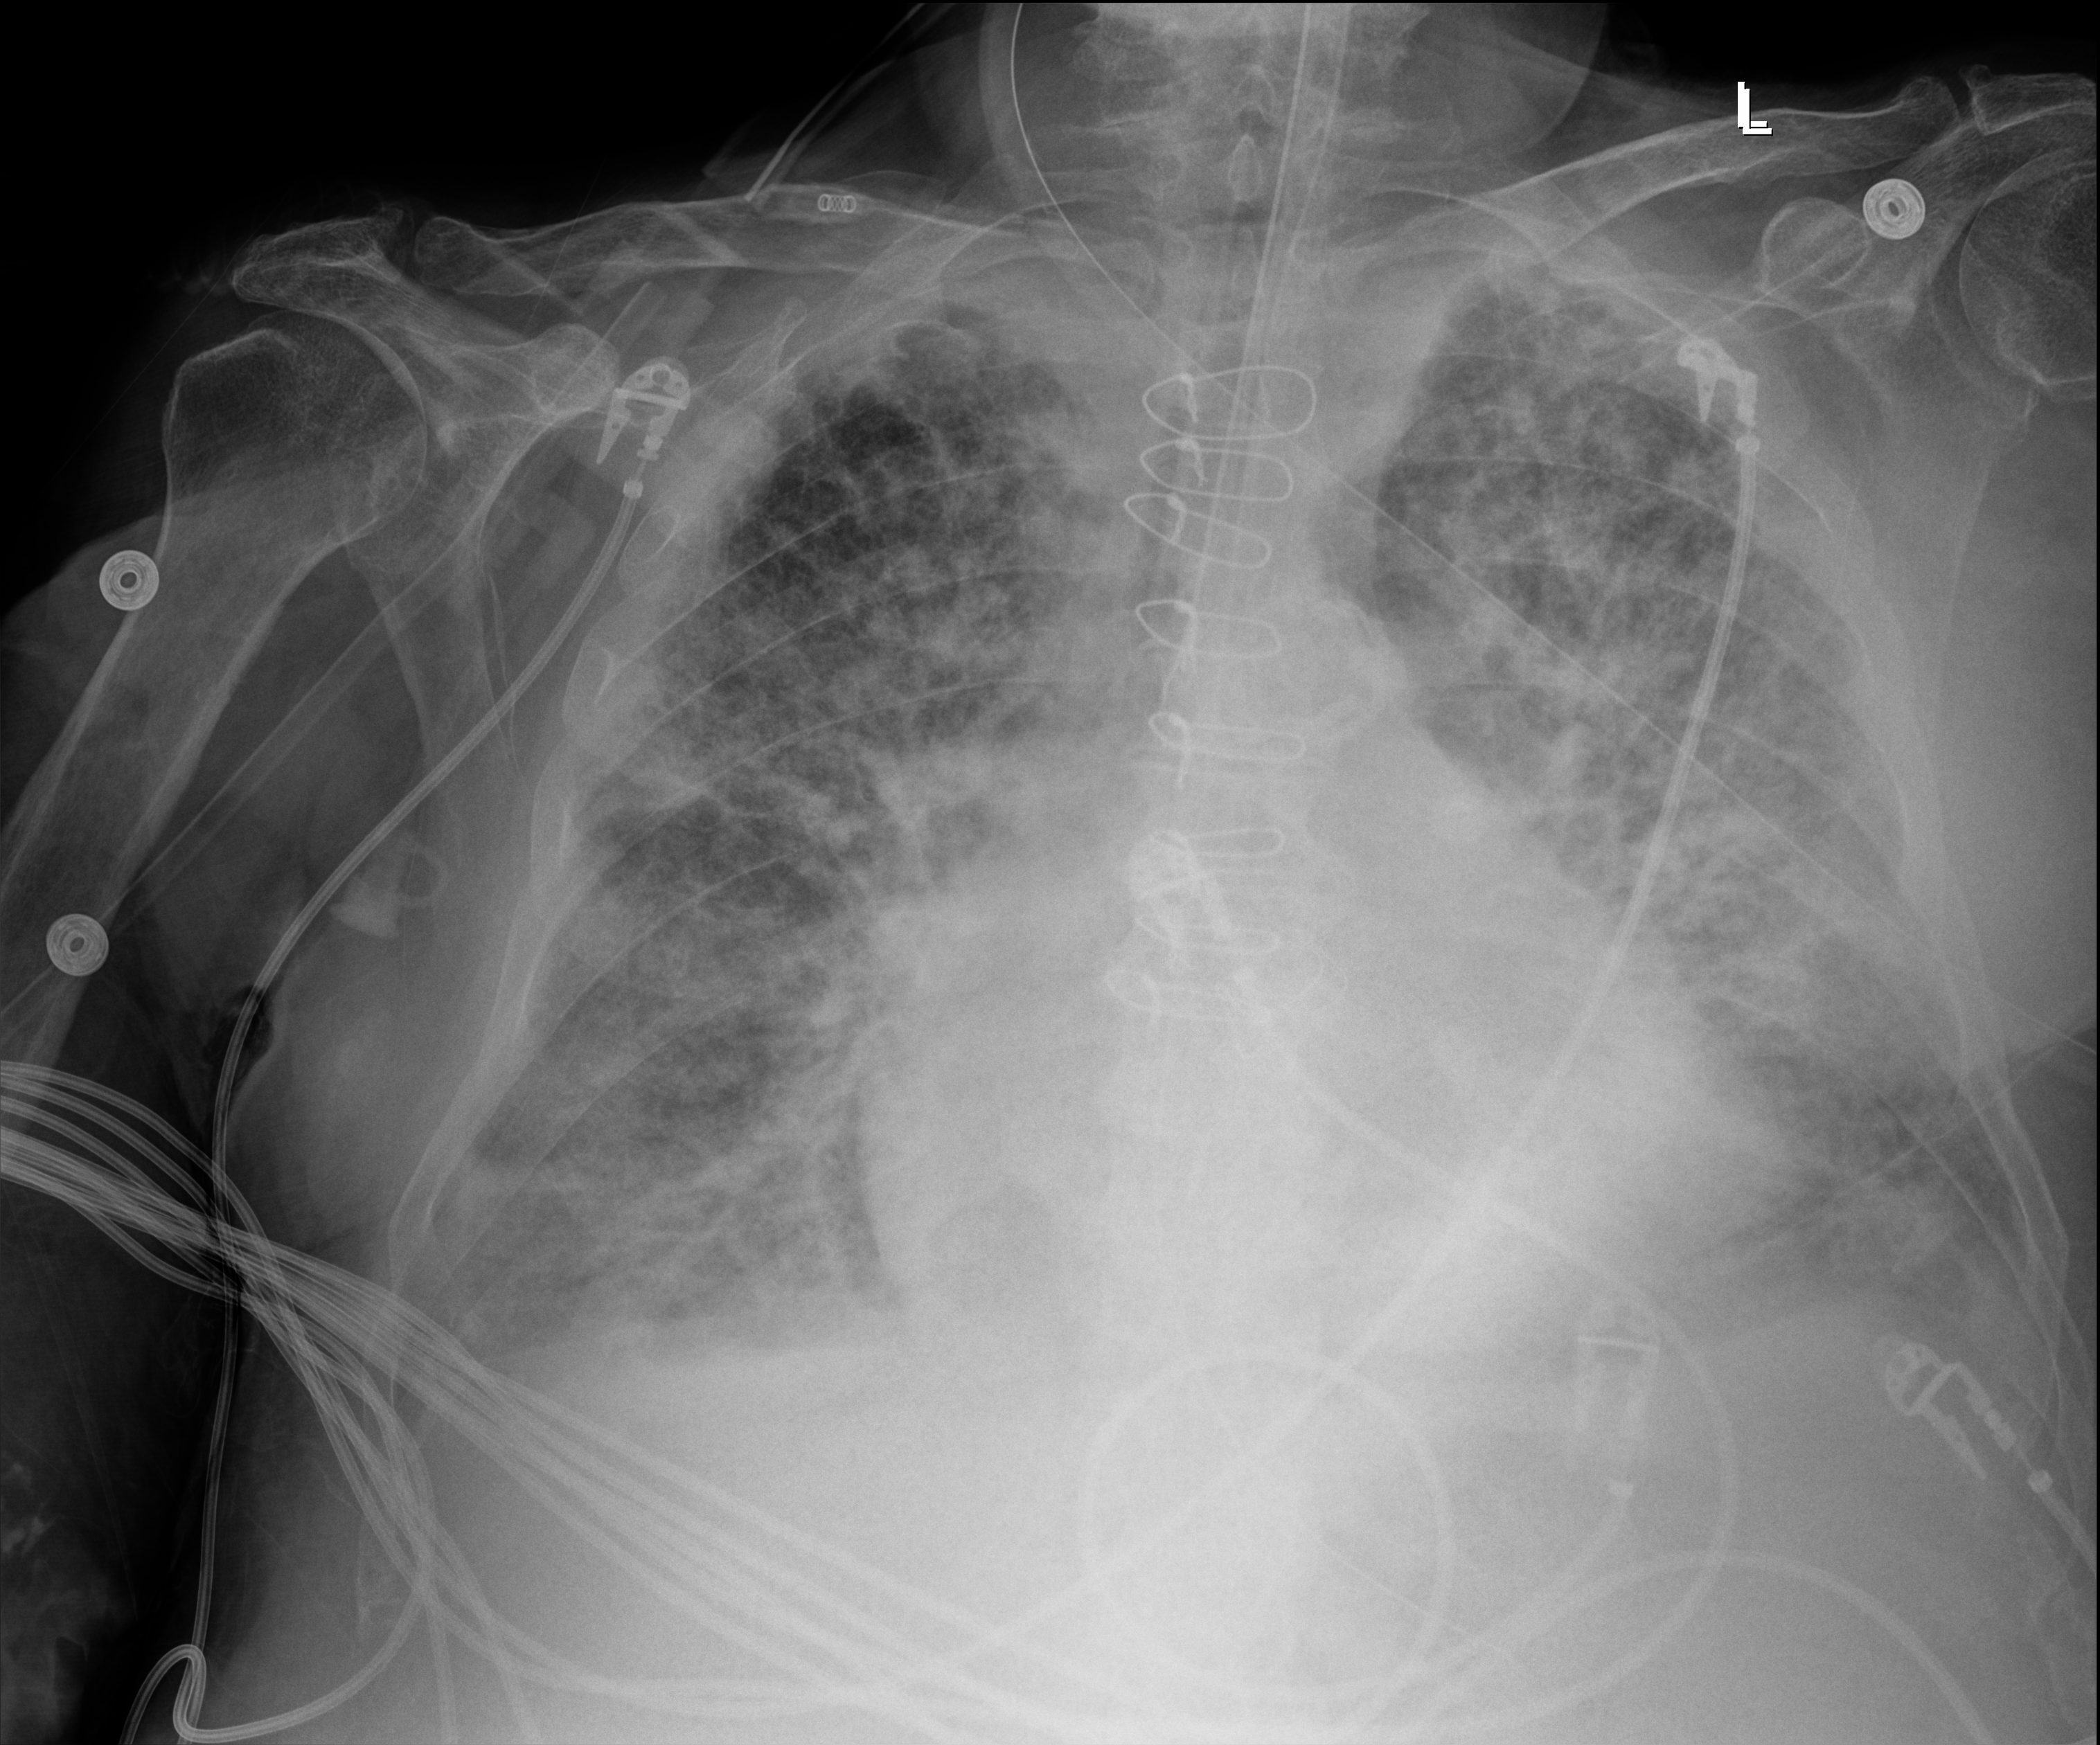
Chest X-ray (portable); anteroposterior (AP) projection. Male patient hospitalised with COVID-19, age 75–90 years.
Hospital-stay facts (about this admission, not read from this image; timing relative to this image not recorded): admitted to intensive care during this hospital stay: yes; mechanically ventilated during this hospital stay: yes.